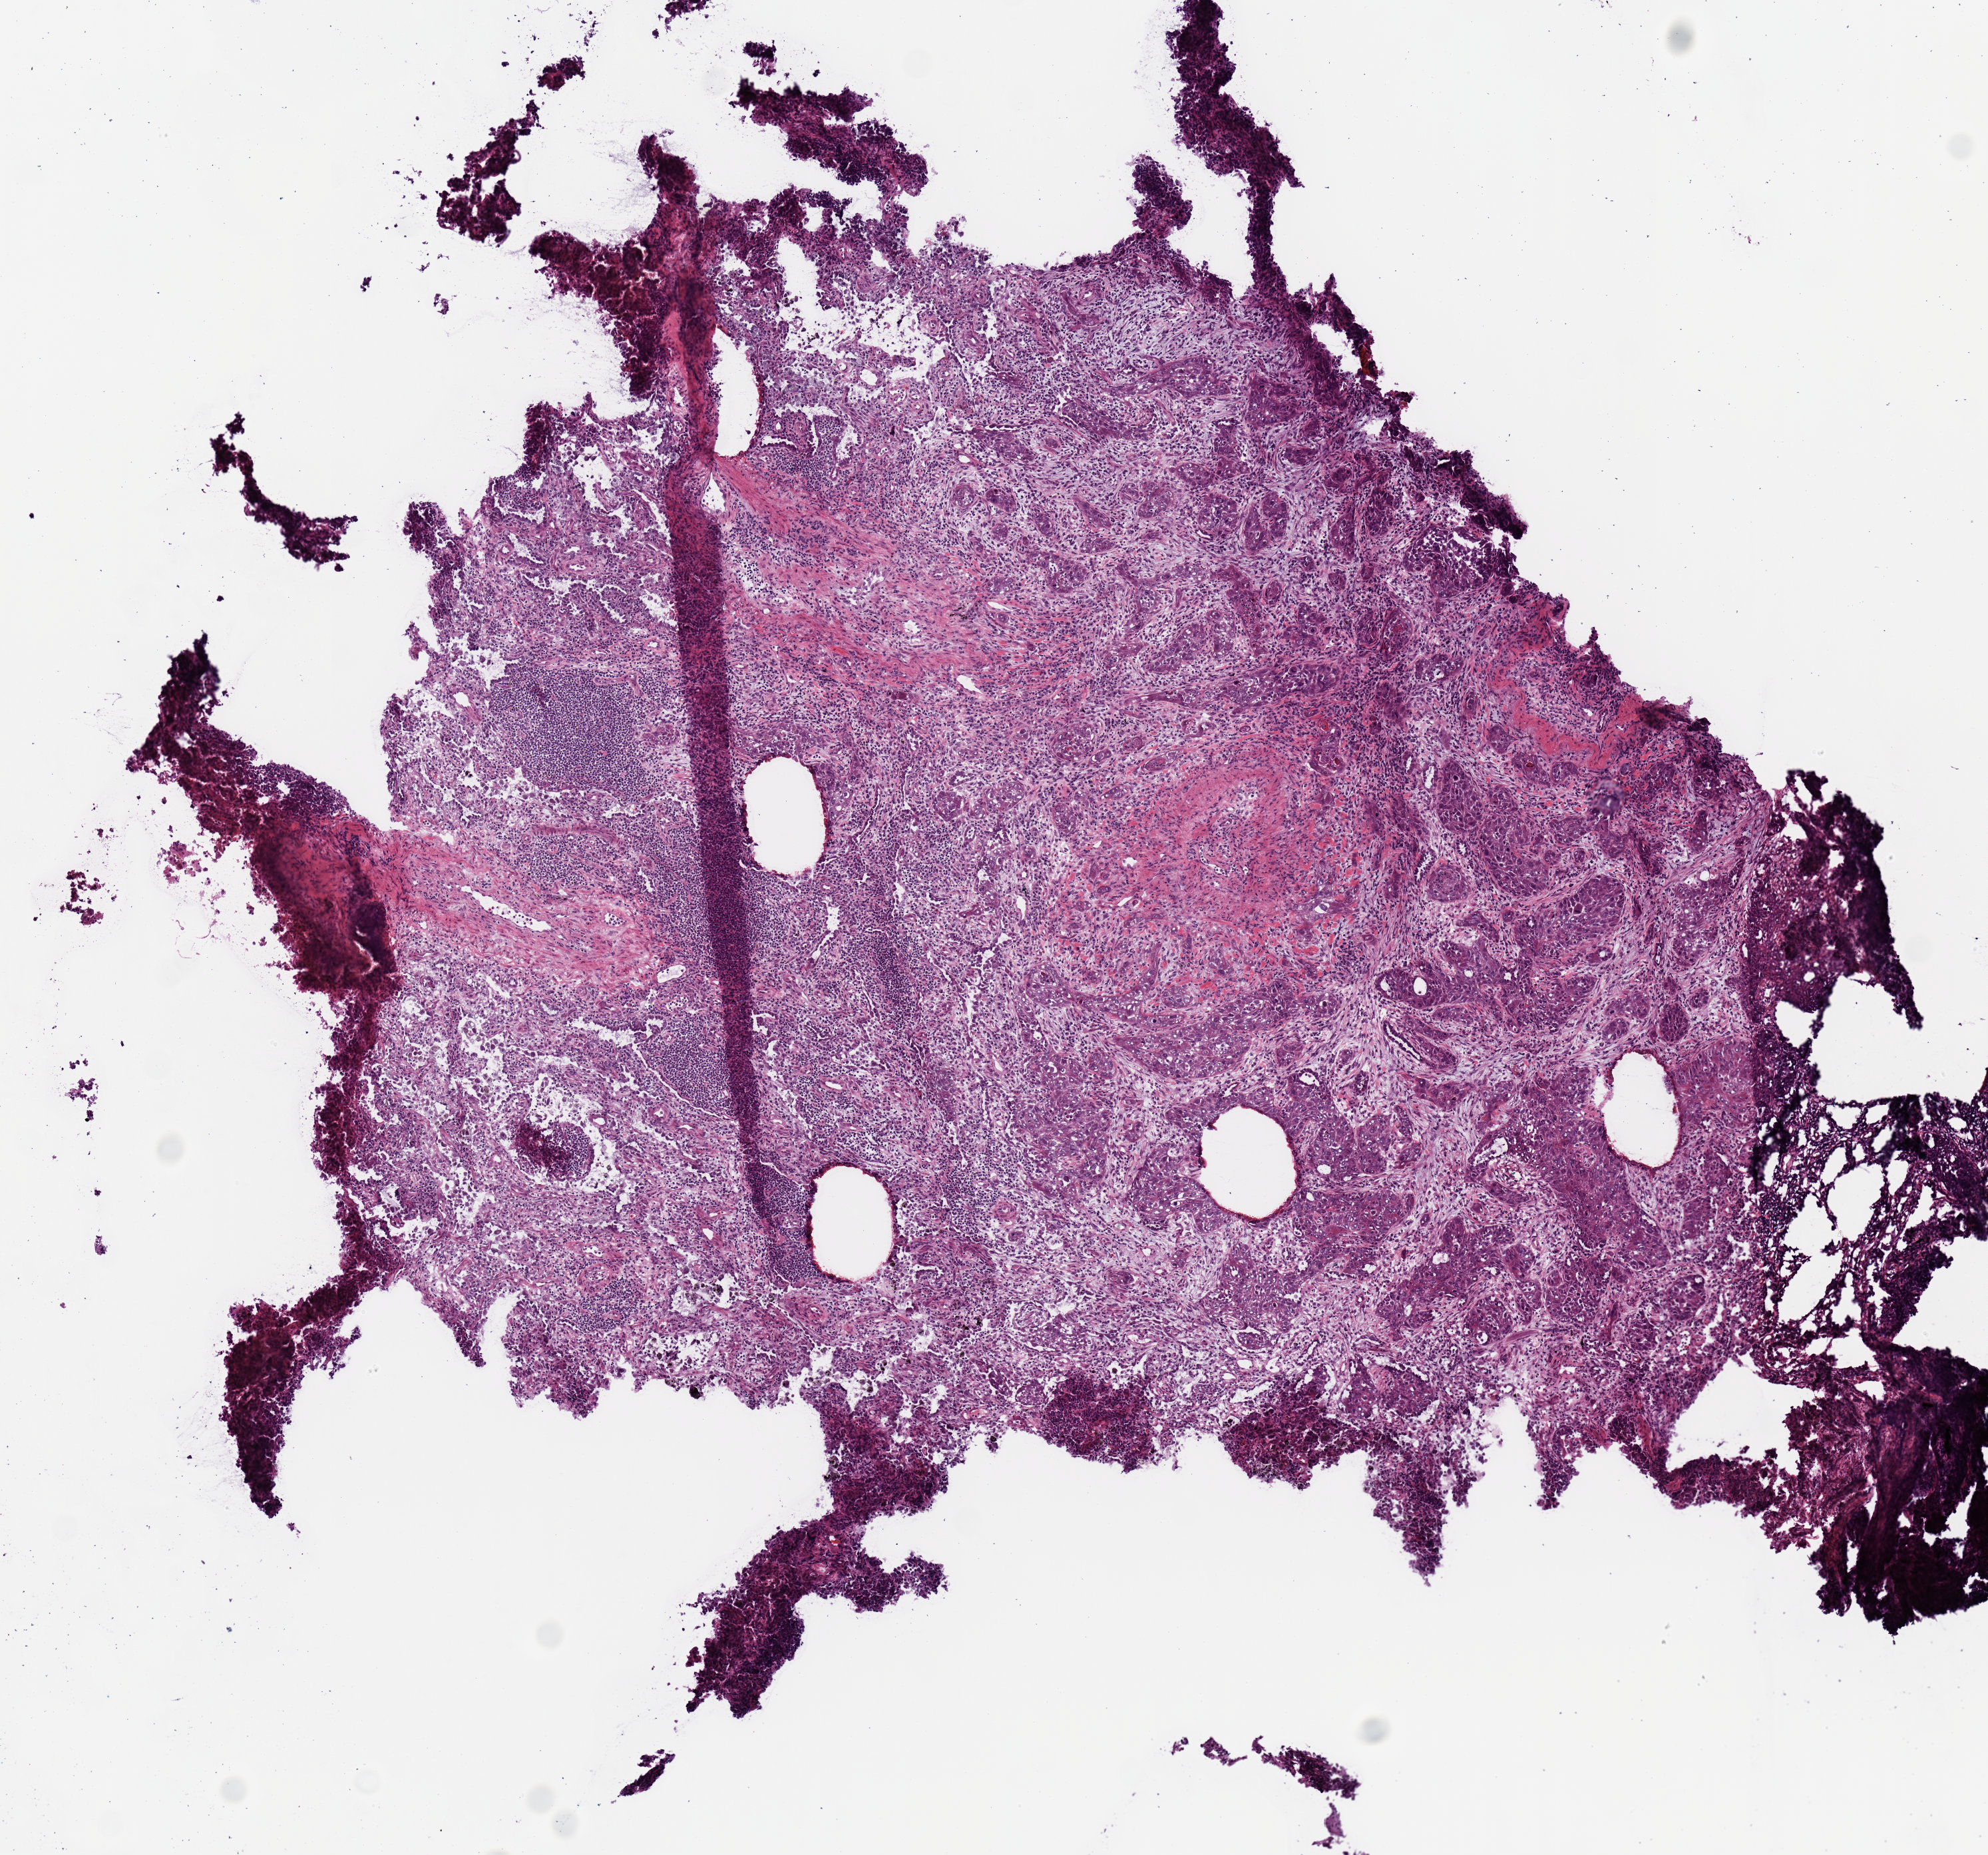
Whole-slide histology image, H&E-stained, low-resolution overview of the scanned area, about 5.9 x 5.5 mm (from a 20x scan), frozen section, primary tumour sample from the lung. Patient: male, age at initial diagnosis 74 years. Composition of this section per pathologist review: tumour cells 75%, tumour nuclei 60%, normal cells 0%, stromal cells 25%, necrosis 0%.
* histologic diagnosis: Squamous cell carcinoma, NOS (upper lobe, lung)
* AJCC pathologic stage: IB